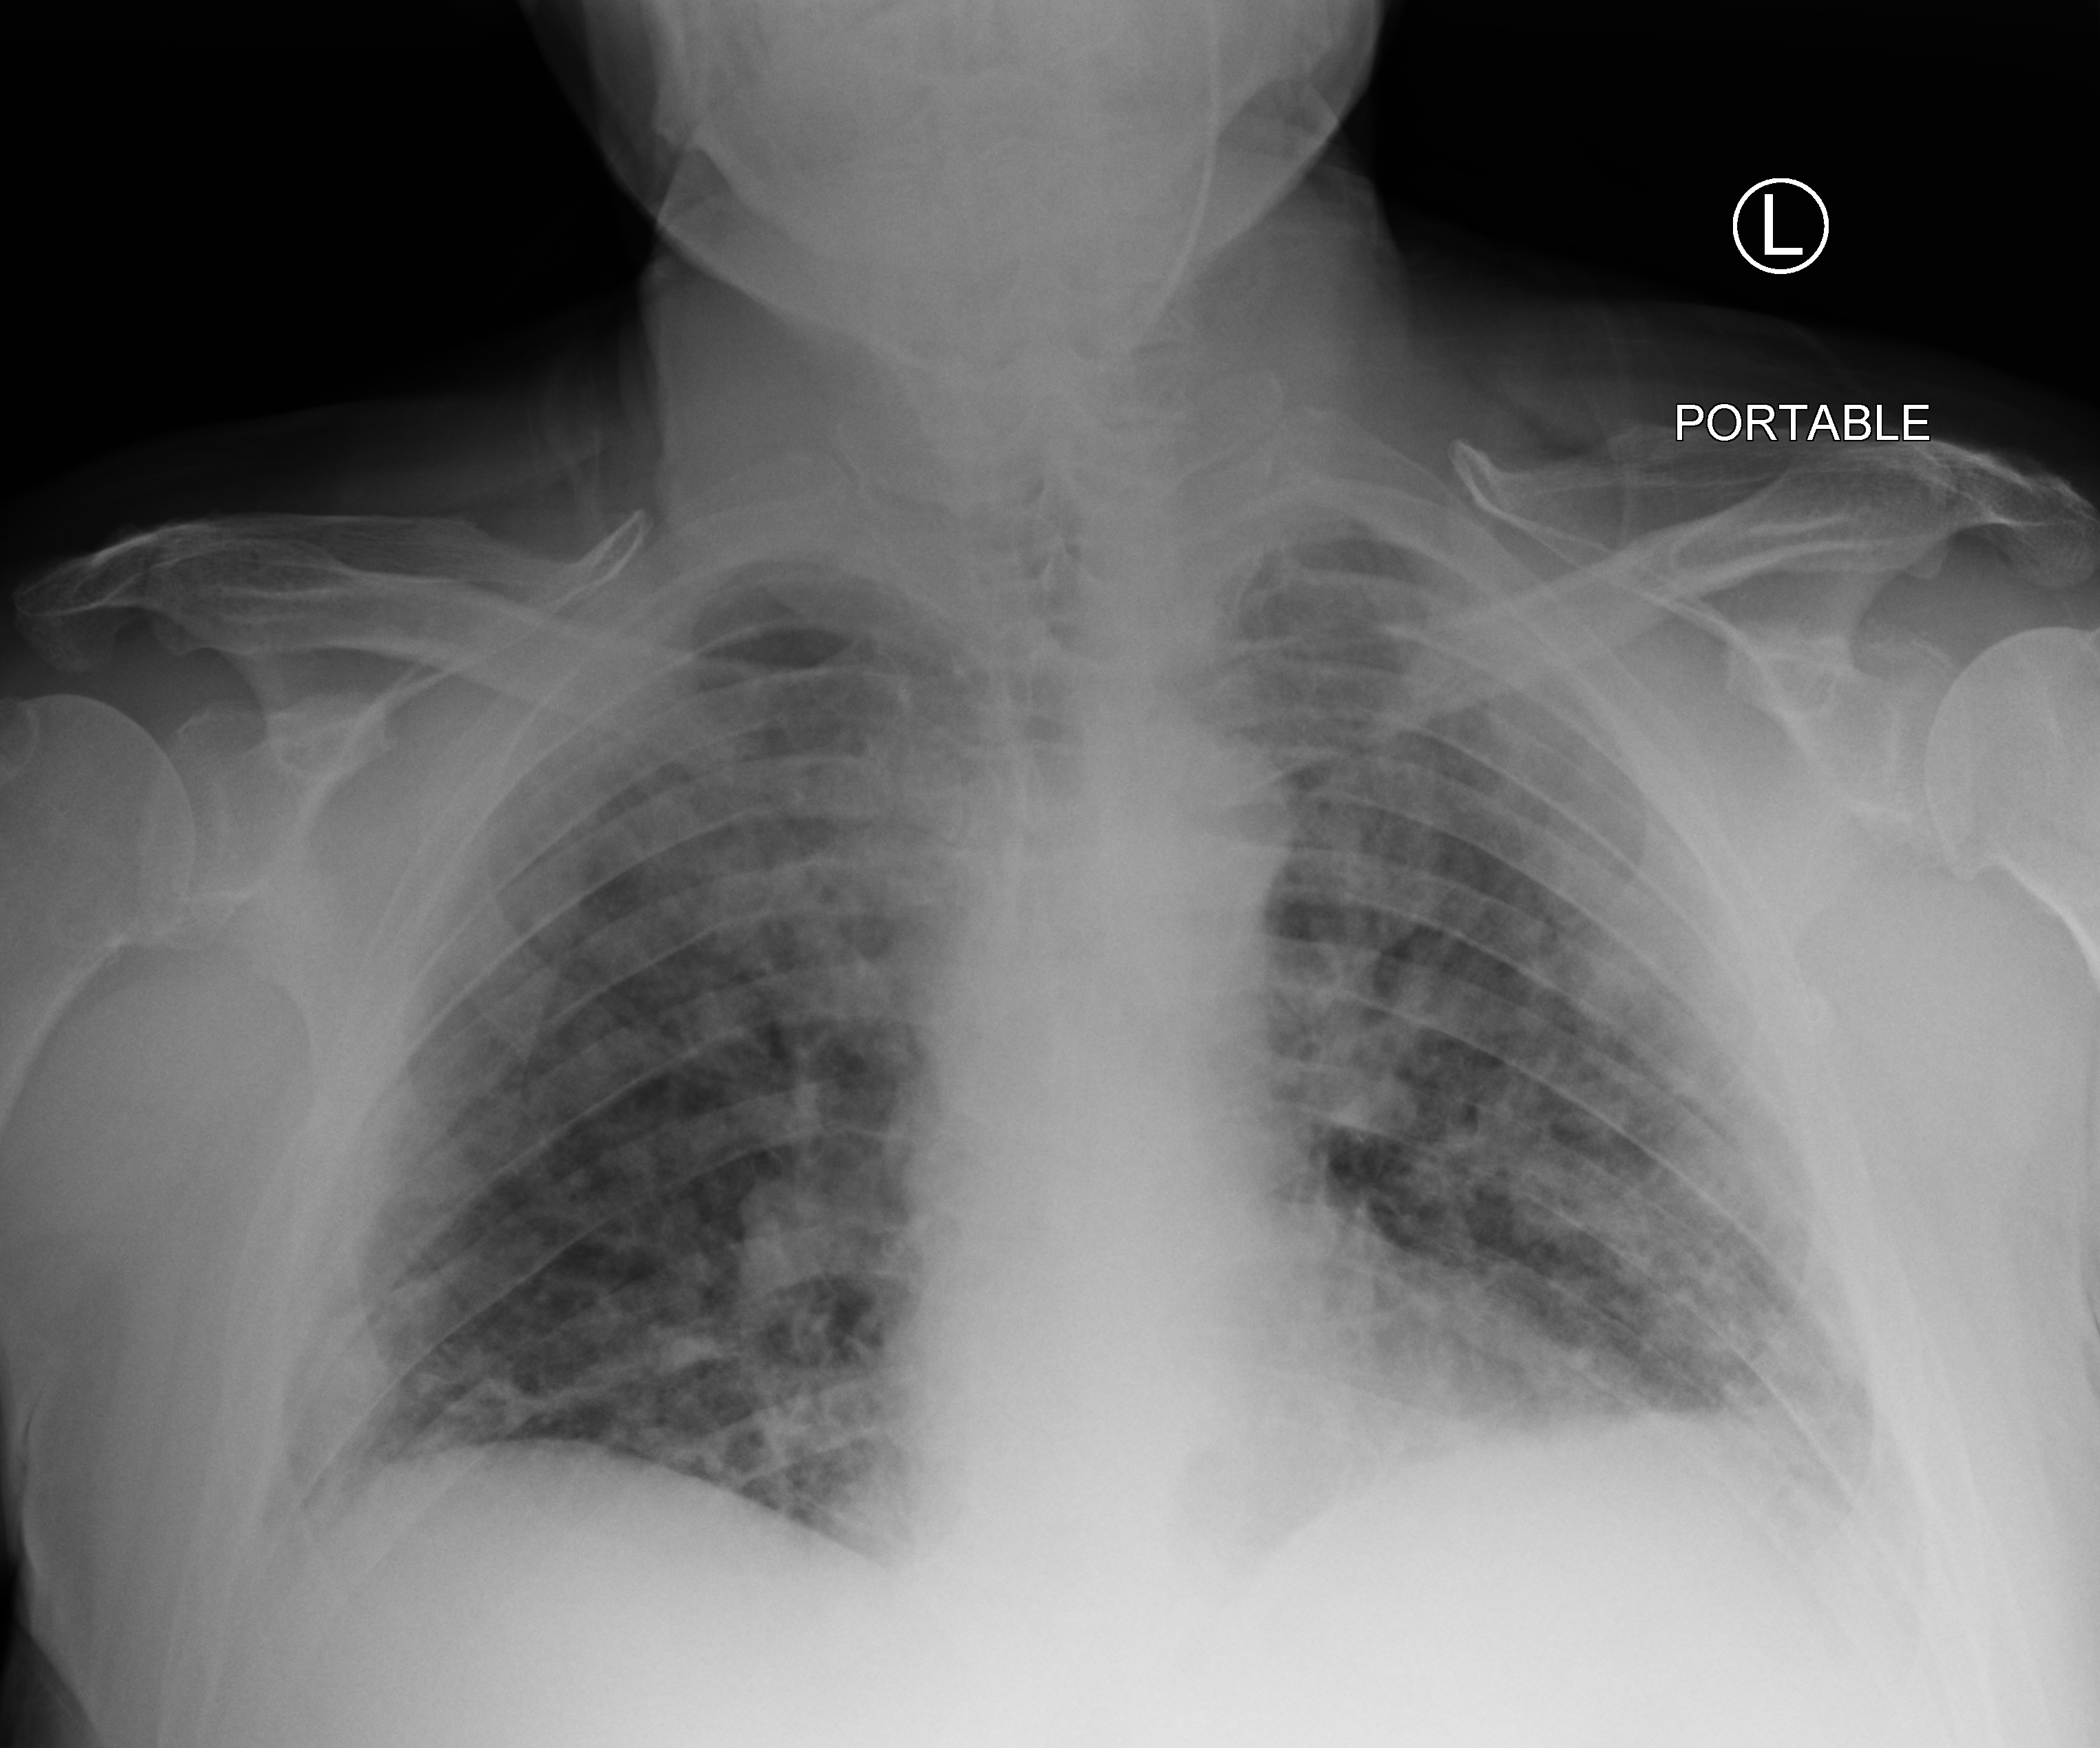
Portable chest radiograph, anteroposterior (AP) projection. Male patient hospitalised with COVID-19, age 60–74 years.
From the hospital-stay record, not from the radiograph (when in the stay this image was taken is not recorded): admitted to intensive care during this hospital stay: no.